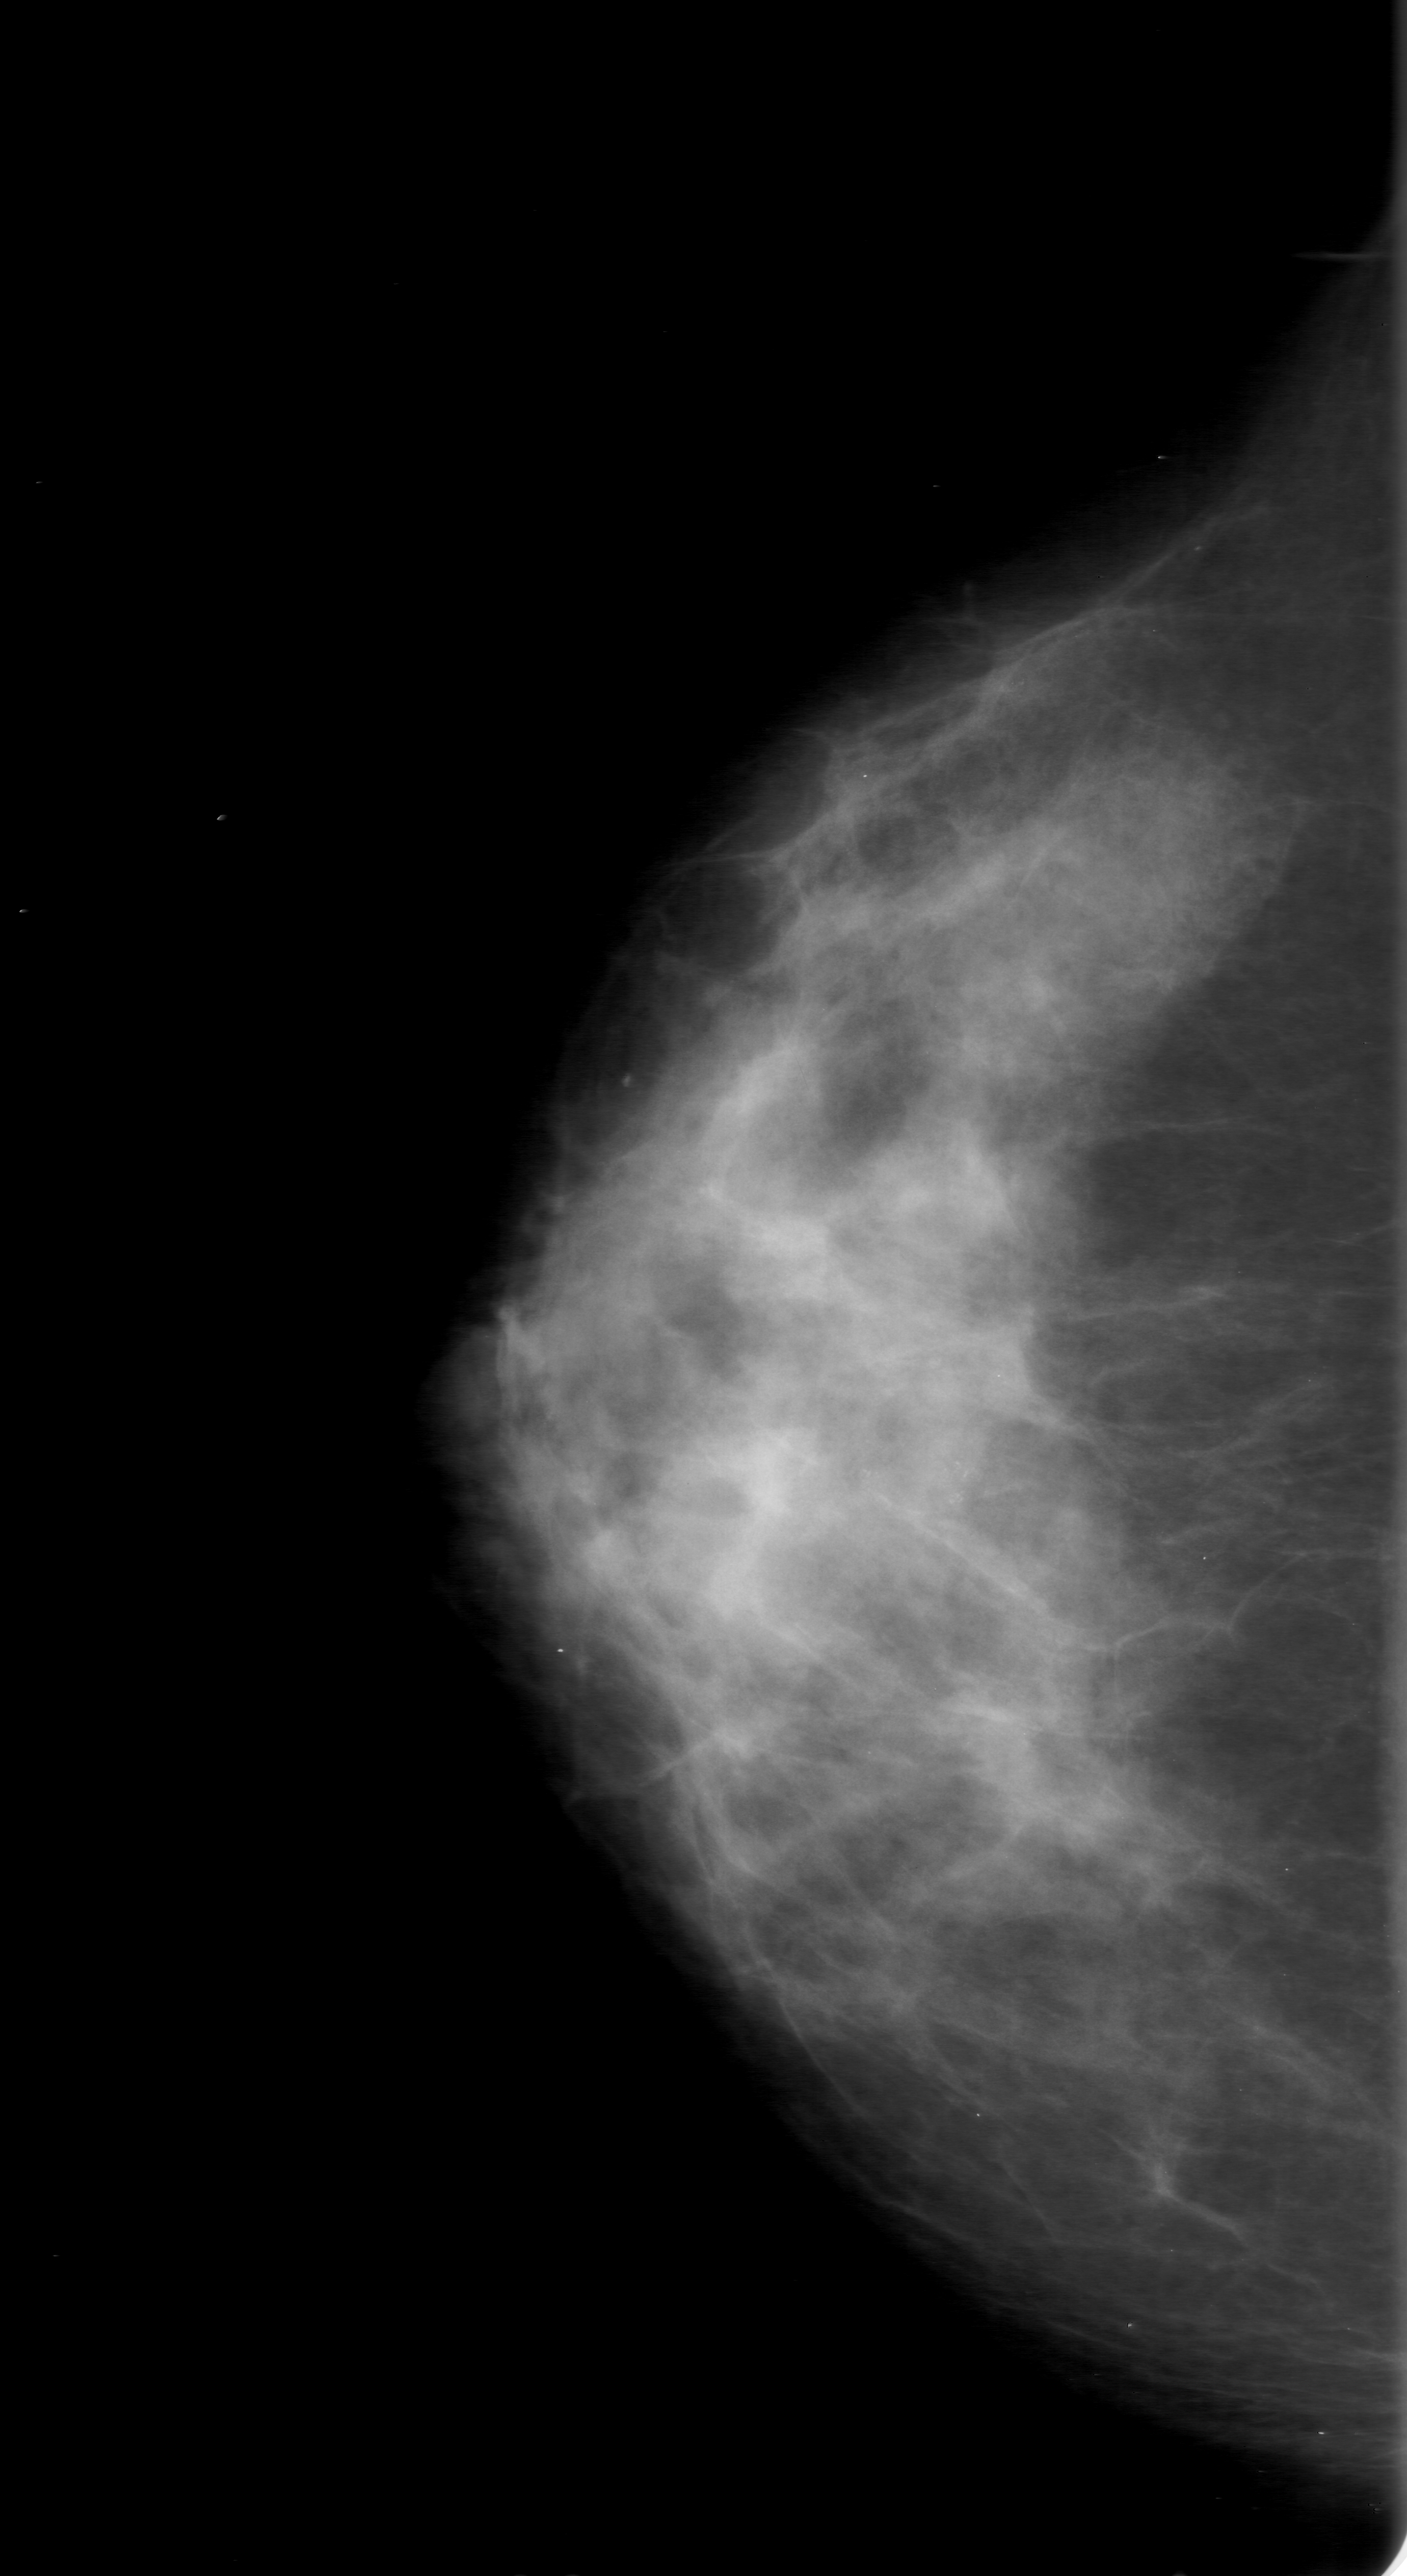
Digitized screen-film mammogram; right breast; craniocaudal (CC) view; BI-RADS breast density category 3 (scale 1–4); 1407 × 2576 image matrix.
Marked abnormalities (boxes around the expert regions of interest):
- calcifications, morphology amorphous, distribution clustered; BI-RADS assessment category 3; subtlety rating 3 on a 1 (subtle) to 5 (obvious) scale; pathology result (as recorded, not read from the image): malignant: box from (x=807, y=1359) to (x=1133, y=1640) px